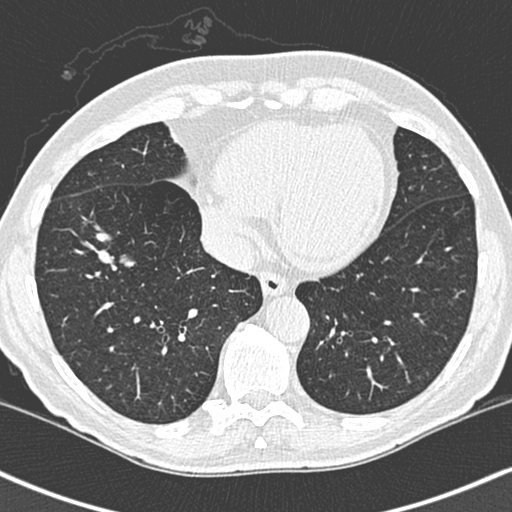
Low-dose screening chest CT, one axial slice. Position 88 of 248 along the scan axis. 120 kVp. Lung window (W 1500 / L -600 HU). 1.3 mm slice thickness. 512 × 512 image matrix.
Annotated regions visible in this slice (manually delineated by an expert):
- lesion 1 (tumor, lower lobe of right lung): bounding box [x1, y1, x2, y2] px = [95, 194, 135, 233]